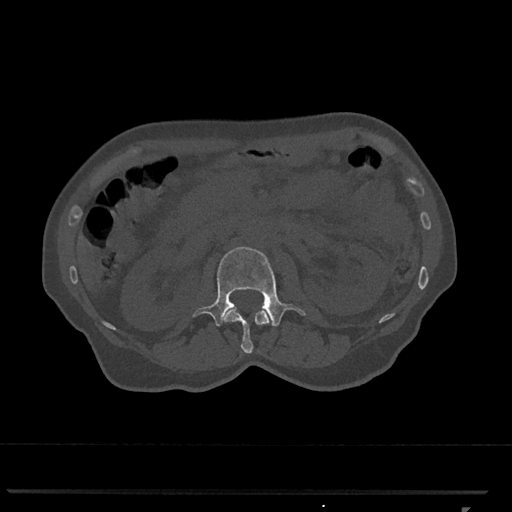
CT including the spine, one axial slice. Position 360 of 793 along the scan axis. 120 kVp. Bone window (W 1800 / L 400 HU). 512 × 512 image matrix, field of view 380 × 380 mm. Patient: female, 62 years. Case-level facts recorded for this patient, not image findings: primary cancer: renal.
Structures marked on this image (semi-automatic segmentation, software-assisted and operator-edited):
- L1 vertebra: bounding box <224,308,272,354> (left, top, right, bottom; pixels)
- L2 vertebra: <193,247,306,327>